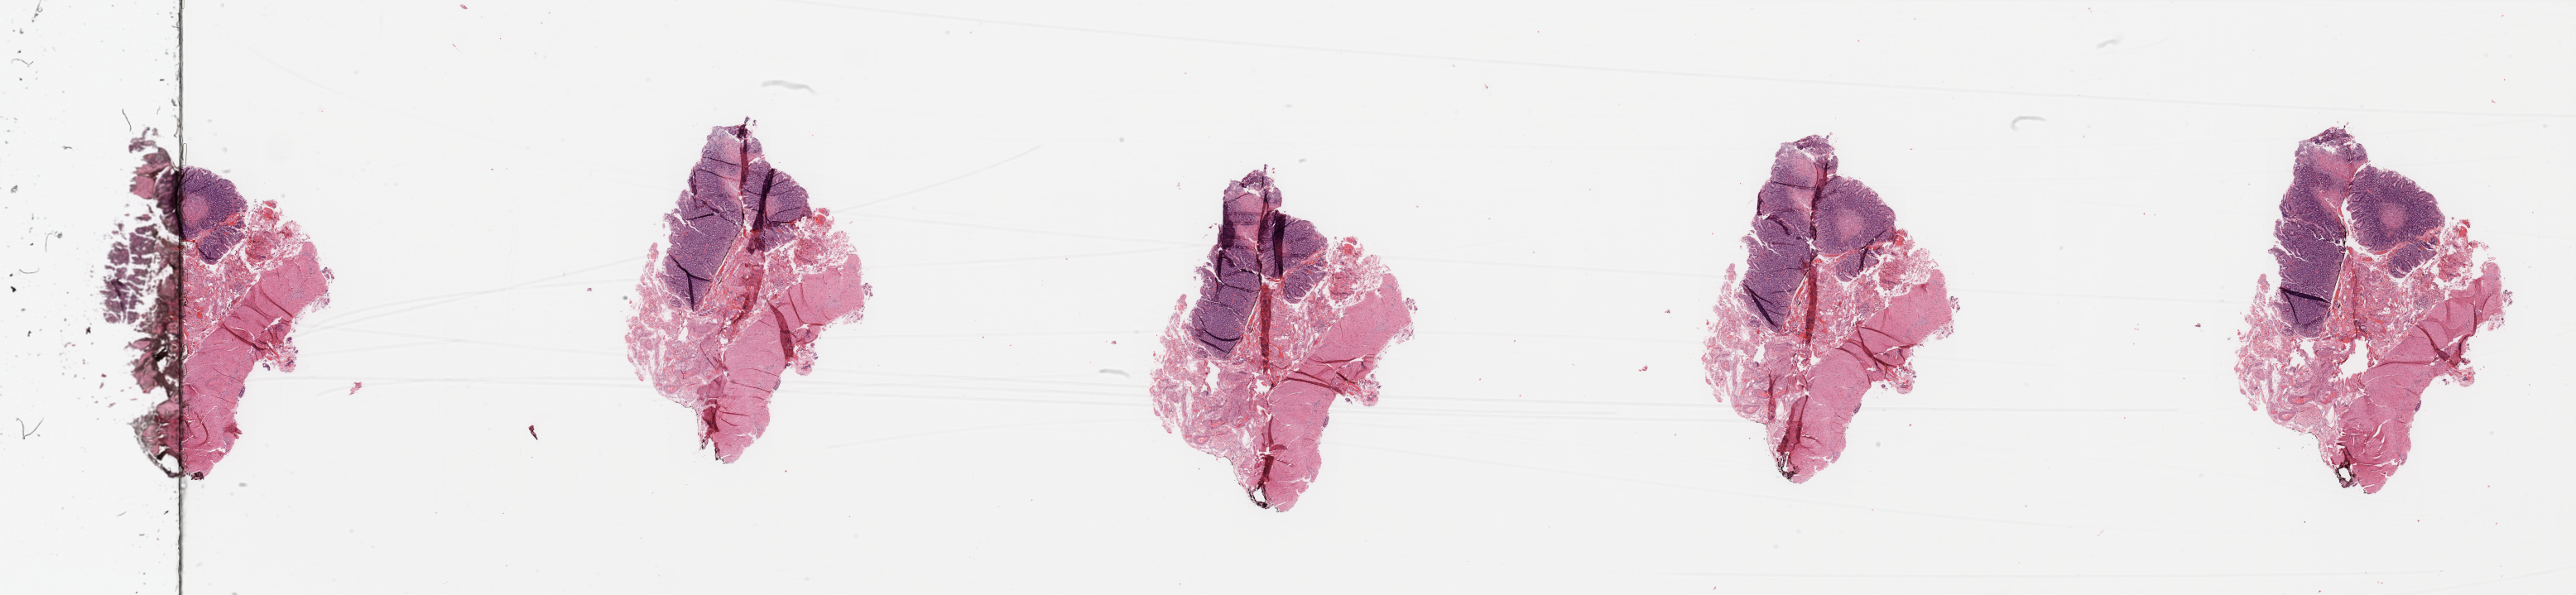
Whole-slide histology image, Hematoxylin and eosin (H&E) stained — whole scanned area (about 49.2 x 11.4 mm, from a 20x scan) shown as a low-resolution overview. Normal (non-tumour) tissue sample, sampled site: pancreas. 77-year-old male patient.
• this section: normal (non-tumour) tissue from the same patient
• patient diagnosis: Infiltrating duct carcinoma, NOS